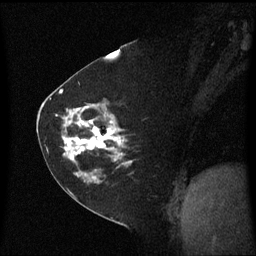
Breast MRI (dynamic contrast-enhanced), one sagittal slice. Dynamic contrast-enhanced series, image 2 of 3 at this slice position (ordered by acquisition). 1.5 T. TE 4.2 ms, TR 8.4 ms. 2 mm slice thickness. 256 × 256 image matrix, field of view 210 × 210 mm. Patient: female, 60 years. Case-level facts recorded for this patient, not image findings: setting: breast cancer imaged before/during neoadjuvant chemotherapy; receptor status: triple-negative.
Annotated regions visible in this slice (semi-automatic segmentation, software-assisted and operator-edited):
- analysis volume of interest (the breast-tissue region the enhancement analysis was run in; not a lesion): box from (x=45, y=99) to (x=134, y=182) px
- tumour enhancement mask (voxels above the 70 % enhancement threshold inside the analysis volume of interest): (x=64, y=107)–(x=133, y=164)